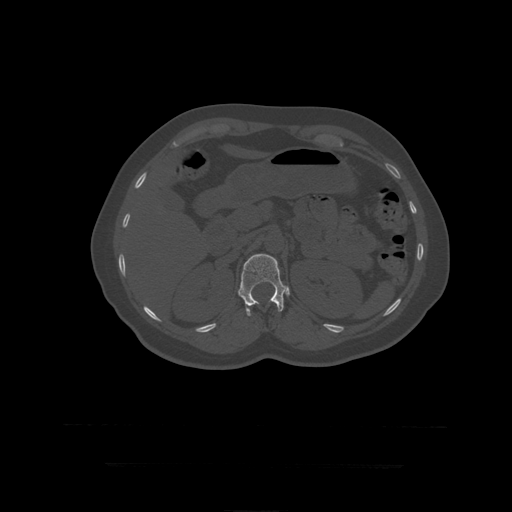
CT including the spine, one axial slice; slice 180 of 399 in the series (ordered by position); reconstruction kernel STANDARD; bone window (W 1800 / L 400 HU); 512 × 512 image matrix, field of view 450 × 450 mm. Patient age 41 years. Case-level facts recorded for this patient, not image findings: primary cancer: breast.
Structures marked on this image (semi-automatic segmentation, software-assisted and operator-edited):
- L1 vertebra: box from (x=238, y=254) to (x=285, y=316) px
- T12 vertebra: (x=249, y=306)–(x=252, y=311)